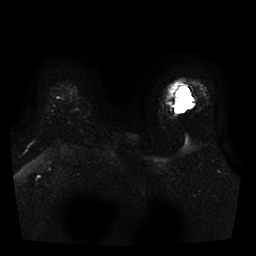
Breast MRI, one axial slice. Position 31 of 41 along the scan axis. Diffusion-weighted series; image 2 of 3 stored at this slice position (different b-values; order by instance number). 1.5 T. 256 × 256 image matrix, field of view 330 × 330 mm. Female patient.
Annotated regions visible in this slice (manually delineated by an expert):
- tumour on diffusion-weighted imaging: box from (x=177, y=93) to (x=193, y=110) px